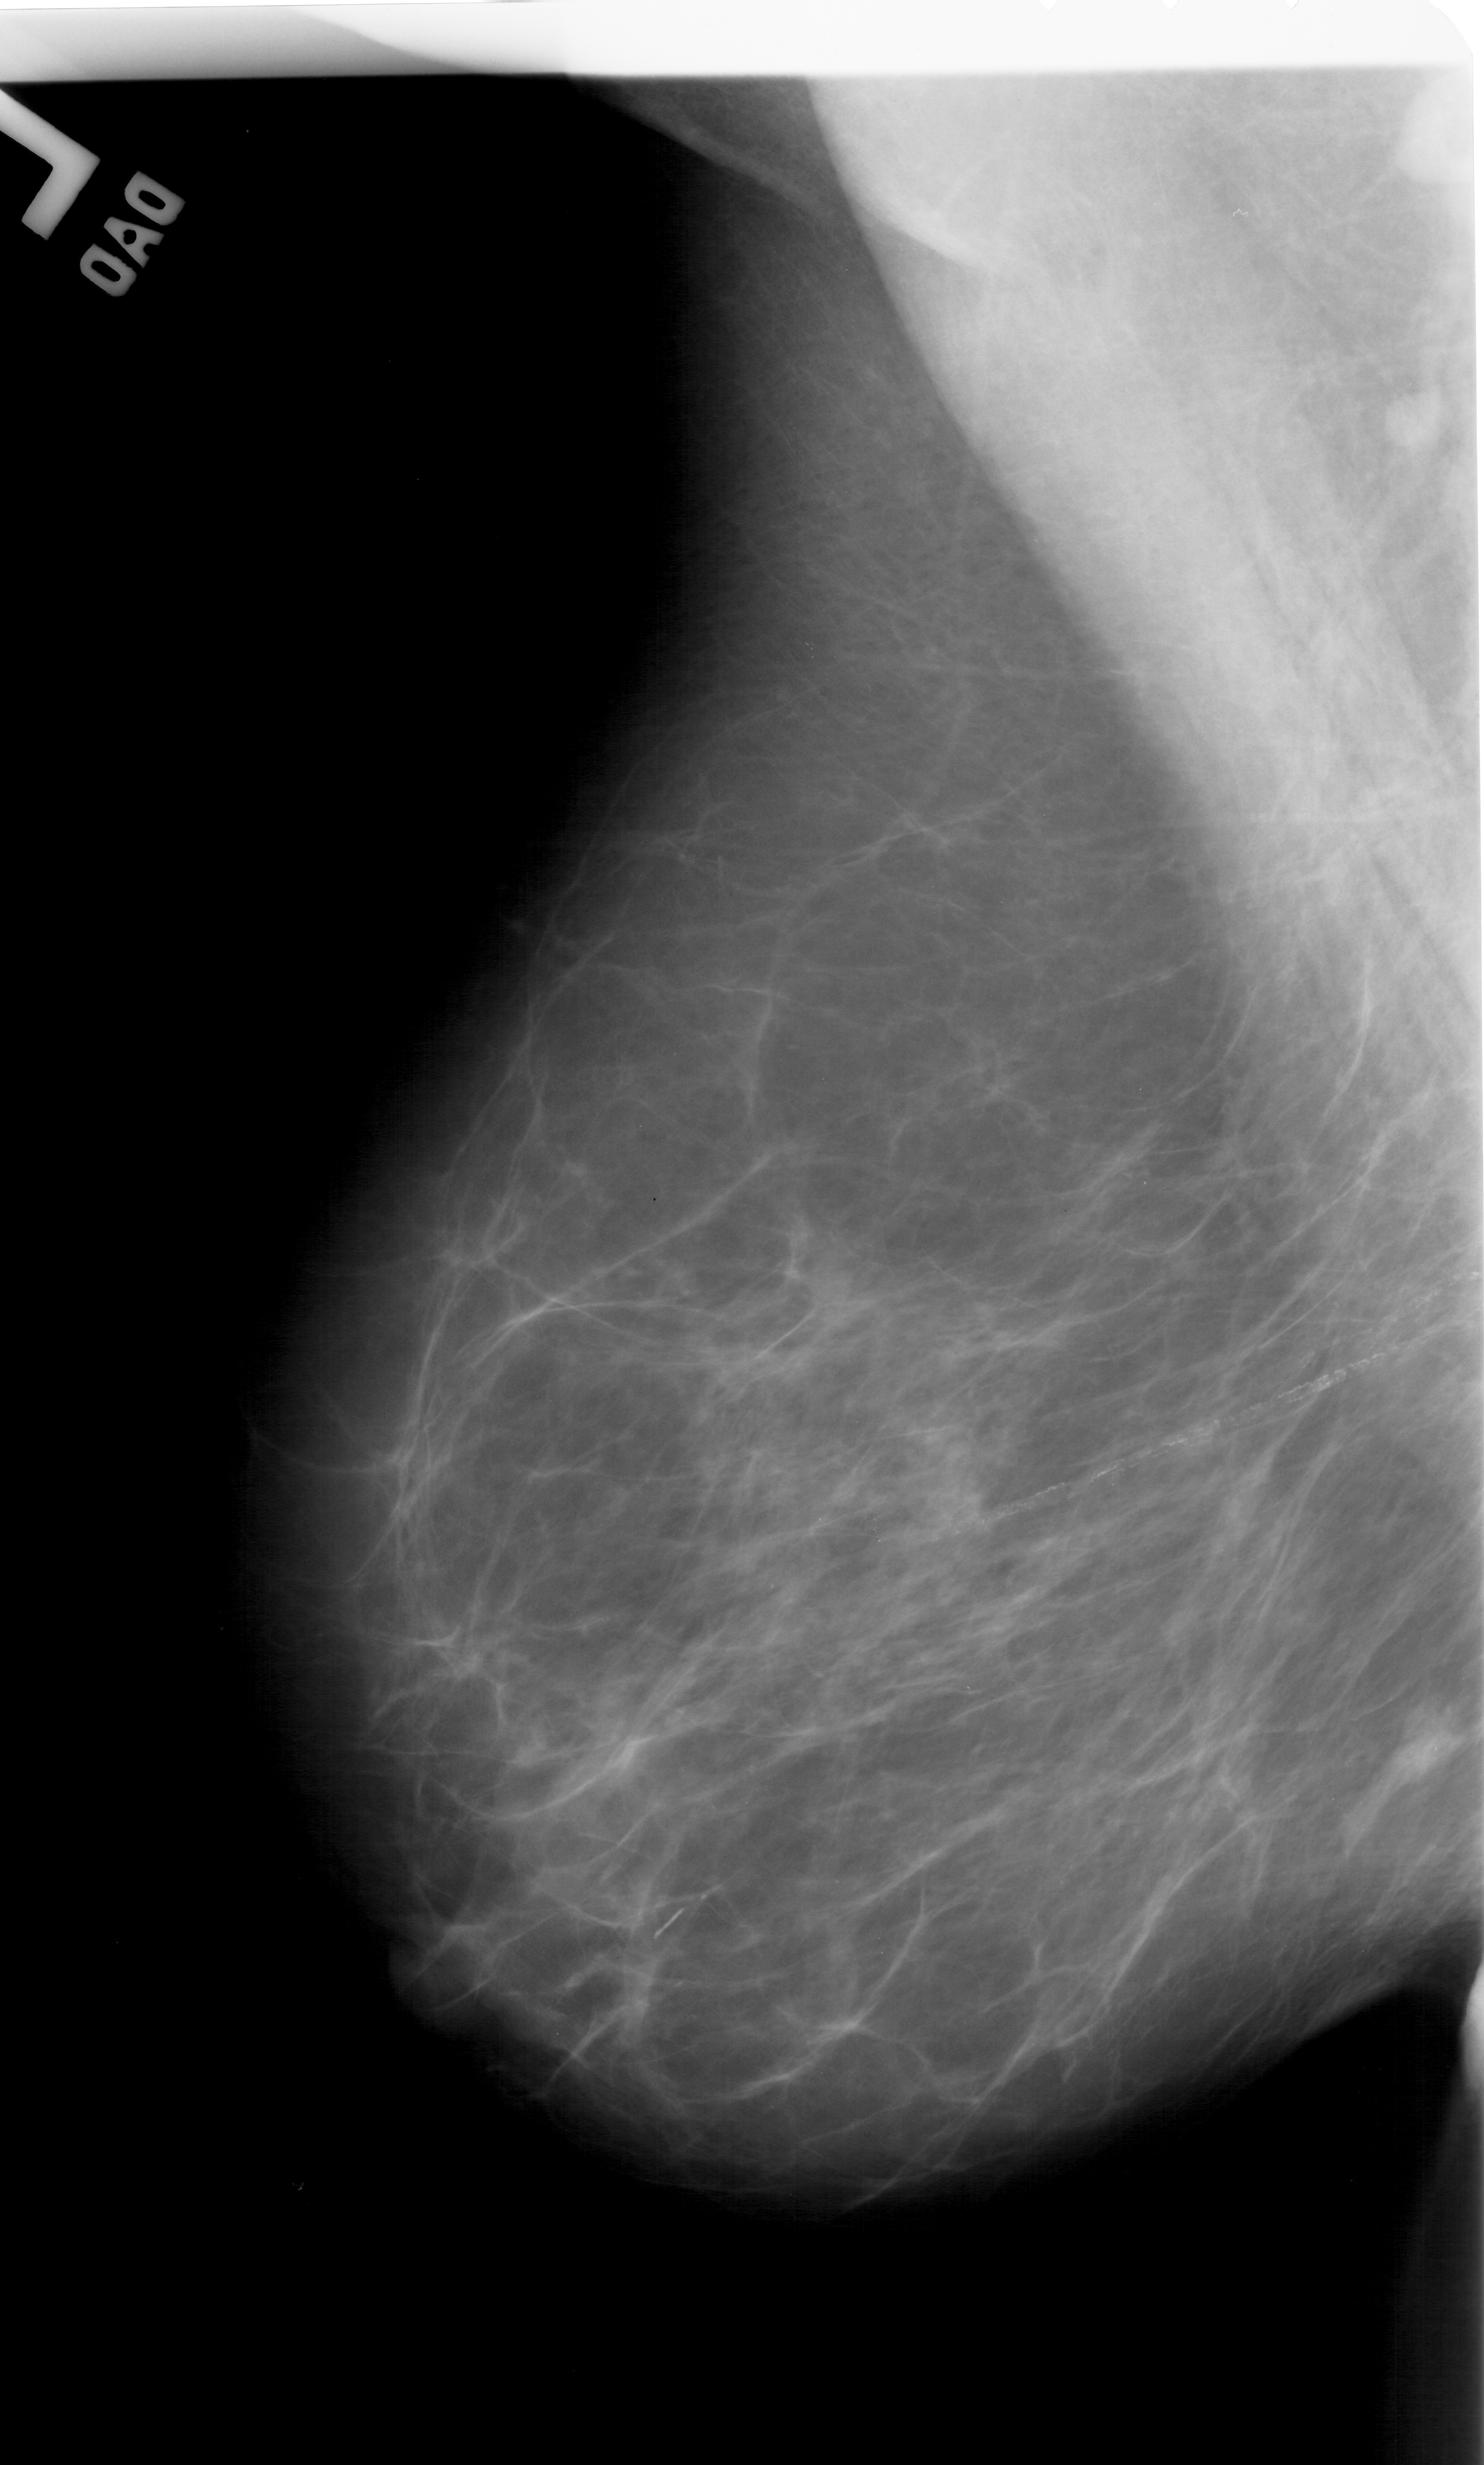
Mammogram (digitized film), left breast, MLO view, BI-RADS breast density category 1 (scale 1–4).
Mass, shape irregular, margins ill defined; BI-RADS assessment category 4; subtlety rating 2 on a 1 (subtle) to 5 (obvious) scale; pathology (as recorded): malignant.